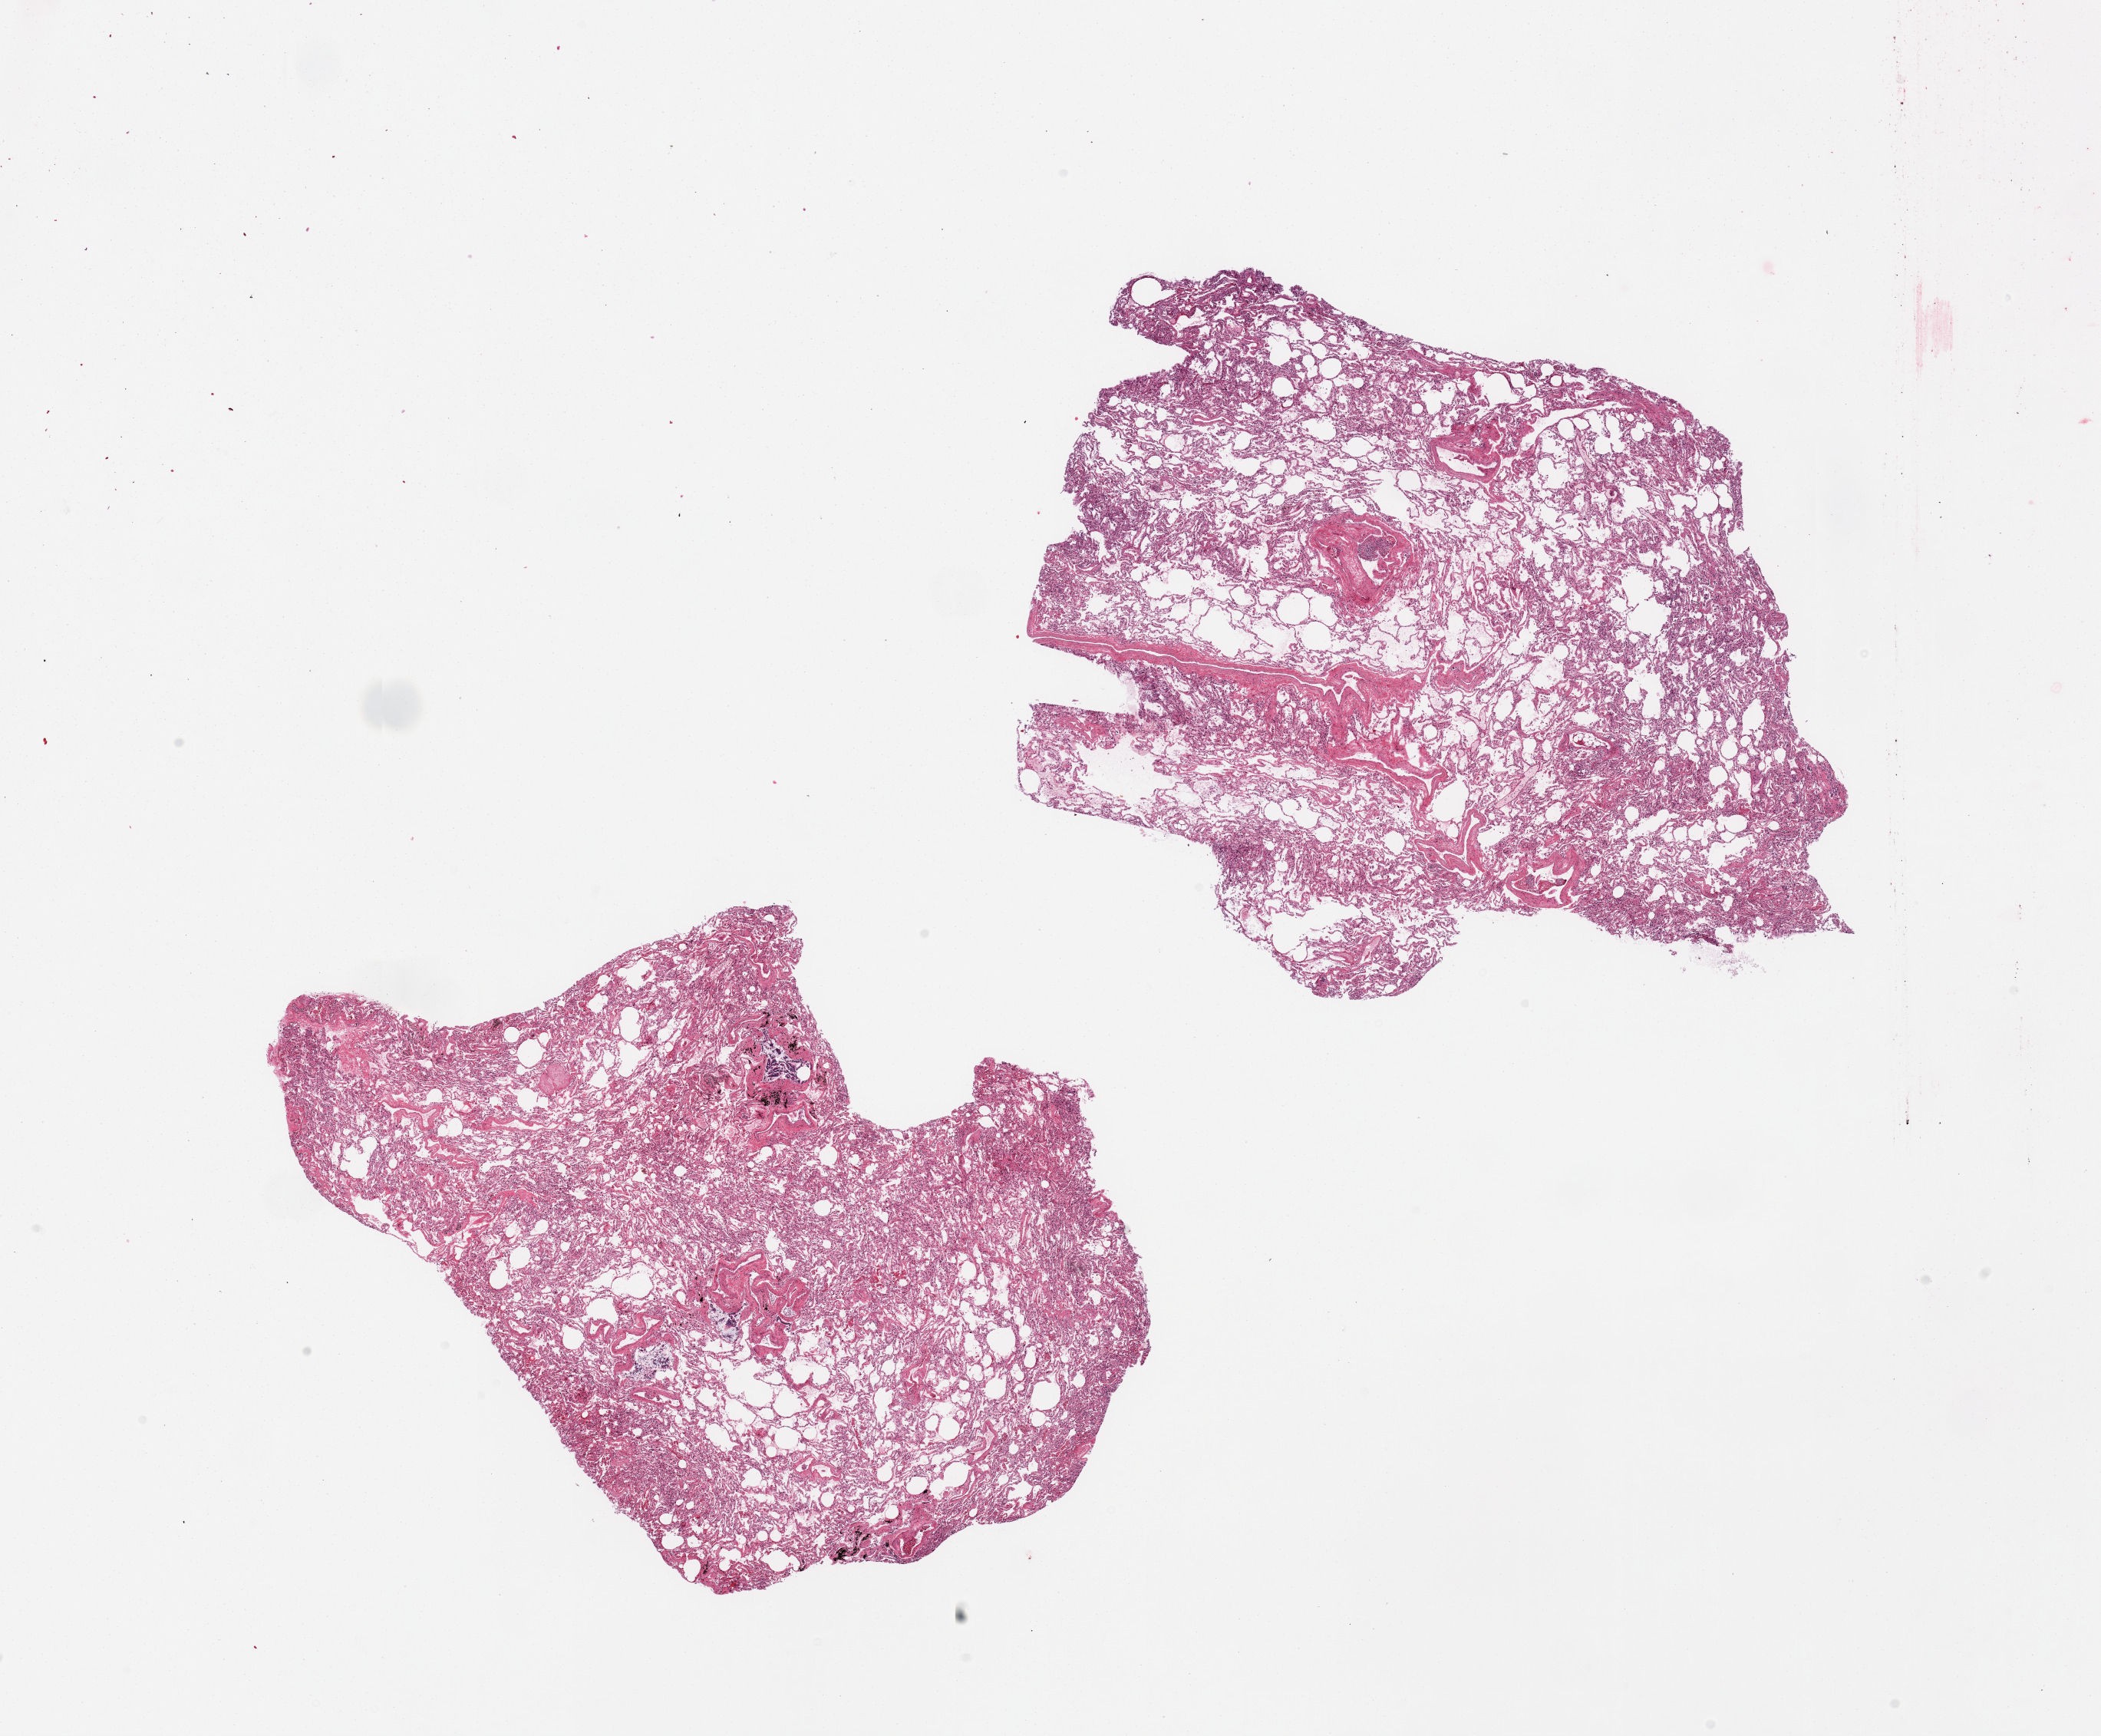
Hematoxylin and eosin (H&E) whole-slide image, whole scanned area (about 21.7 x 17.9 mm) shown as a low-resolution overview; PAXgene-fixed, paraffin-embedded tissue; section of lung (target tissue); donor tissue sample. Donor: male.
Pathologist's review note for this sample: 2 pieces, moderate congestion.